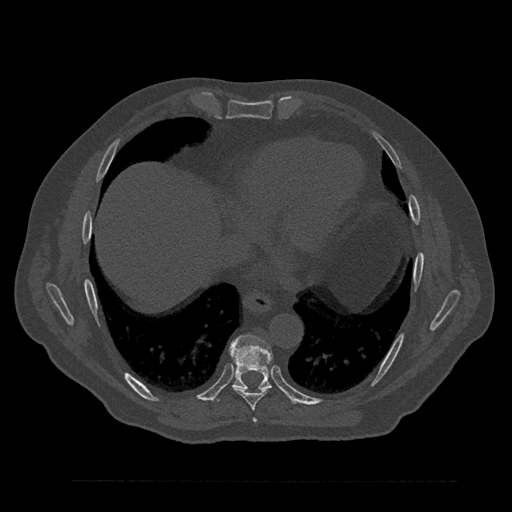
CT including the spine, one axial slice; position 433 of 797 along the scan axis; reconstruction kernel Br40s/3; bone window (W 1800 / L 400 HU); 0.5 mm slice thickness; 512 × 512 image matrix, field of view 430 × 430 mm. Male patient, age 61 years. From the clinical record (not read from this slice): primary cancer: prostate.
Structures marked on this image (semi-automatically segmented with operator editing):
- T7 vertebra: bounding box [x1, y1, x2, y2] px = [253, 419, 256, 422]
- T8 vertebra: [232, 386, 272, 411]
- T9 vertebra: [229, 334, 272, 389]